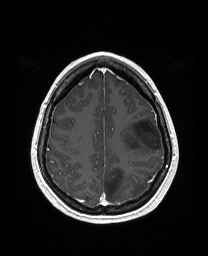
Brain MRI from a brain-tumour surgery series, one axial slice; position 122 of 176 along the scan axis; T1-weighted post-contrast; 1 mm slice thickness; 208 × 256 image matrix, field of view 203 × 250 mm. From the clinical record (not read from this slice): histopathology: Astrocytoma; WHO grade: 3; IDH mutation: yes; tumour location: Left Frontal.
Annotated regions visible in this slice (outlined manually by an expert reader):
- tumour: bounding box (x1, y1, x2, y2) in pixels: (122, 116, 162, 152)